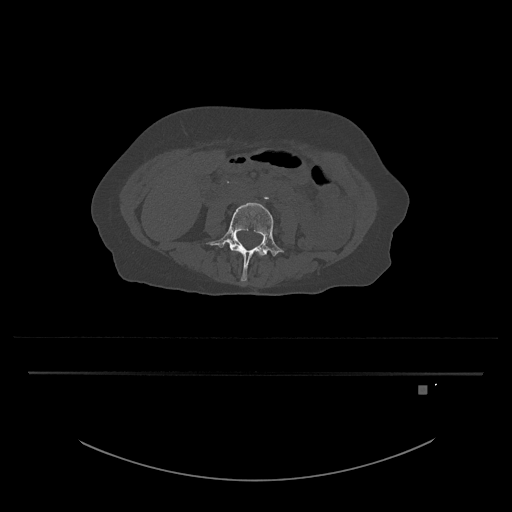
CT including the spine, one axial slice. Position 368 of 797 along the scan axis. Reconstruction kernel Br40s/3. 120 kVp. Bone window (W 1800 / L 400 HU). 0.5 mm slice thickness. 512 × 512 image matrix, field of view 500 × 500 mm. Patient: female, 57 years. From the clinical record (not read from this slice): primary cancer: cervical.
Outlined on this slice (semi-automatic segmentation, software-assisted and operator-edited):
- L3 vertebra: box from (x=258, y=253) to (x=262, y=256) px
- L4 vertebra: (x=206, y=202)–(x=284, y=282)